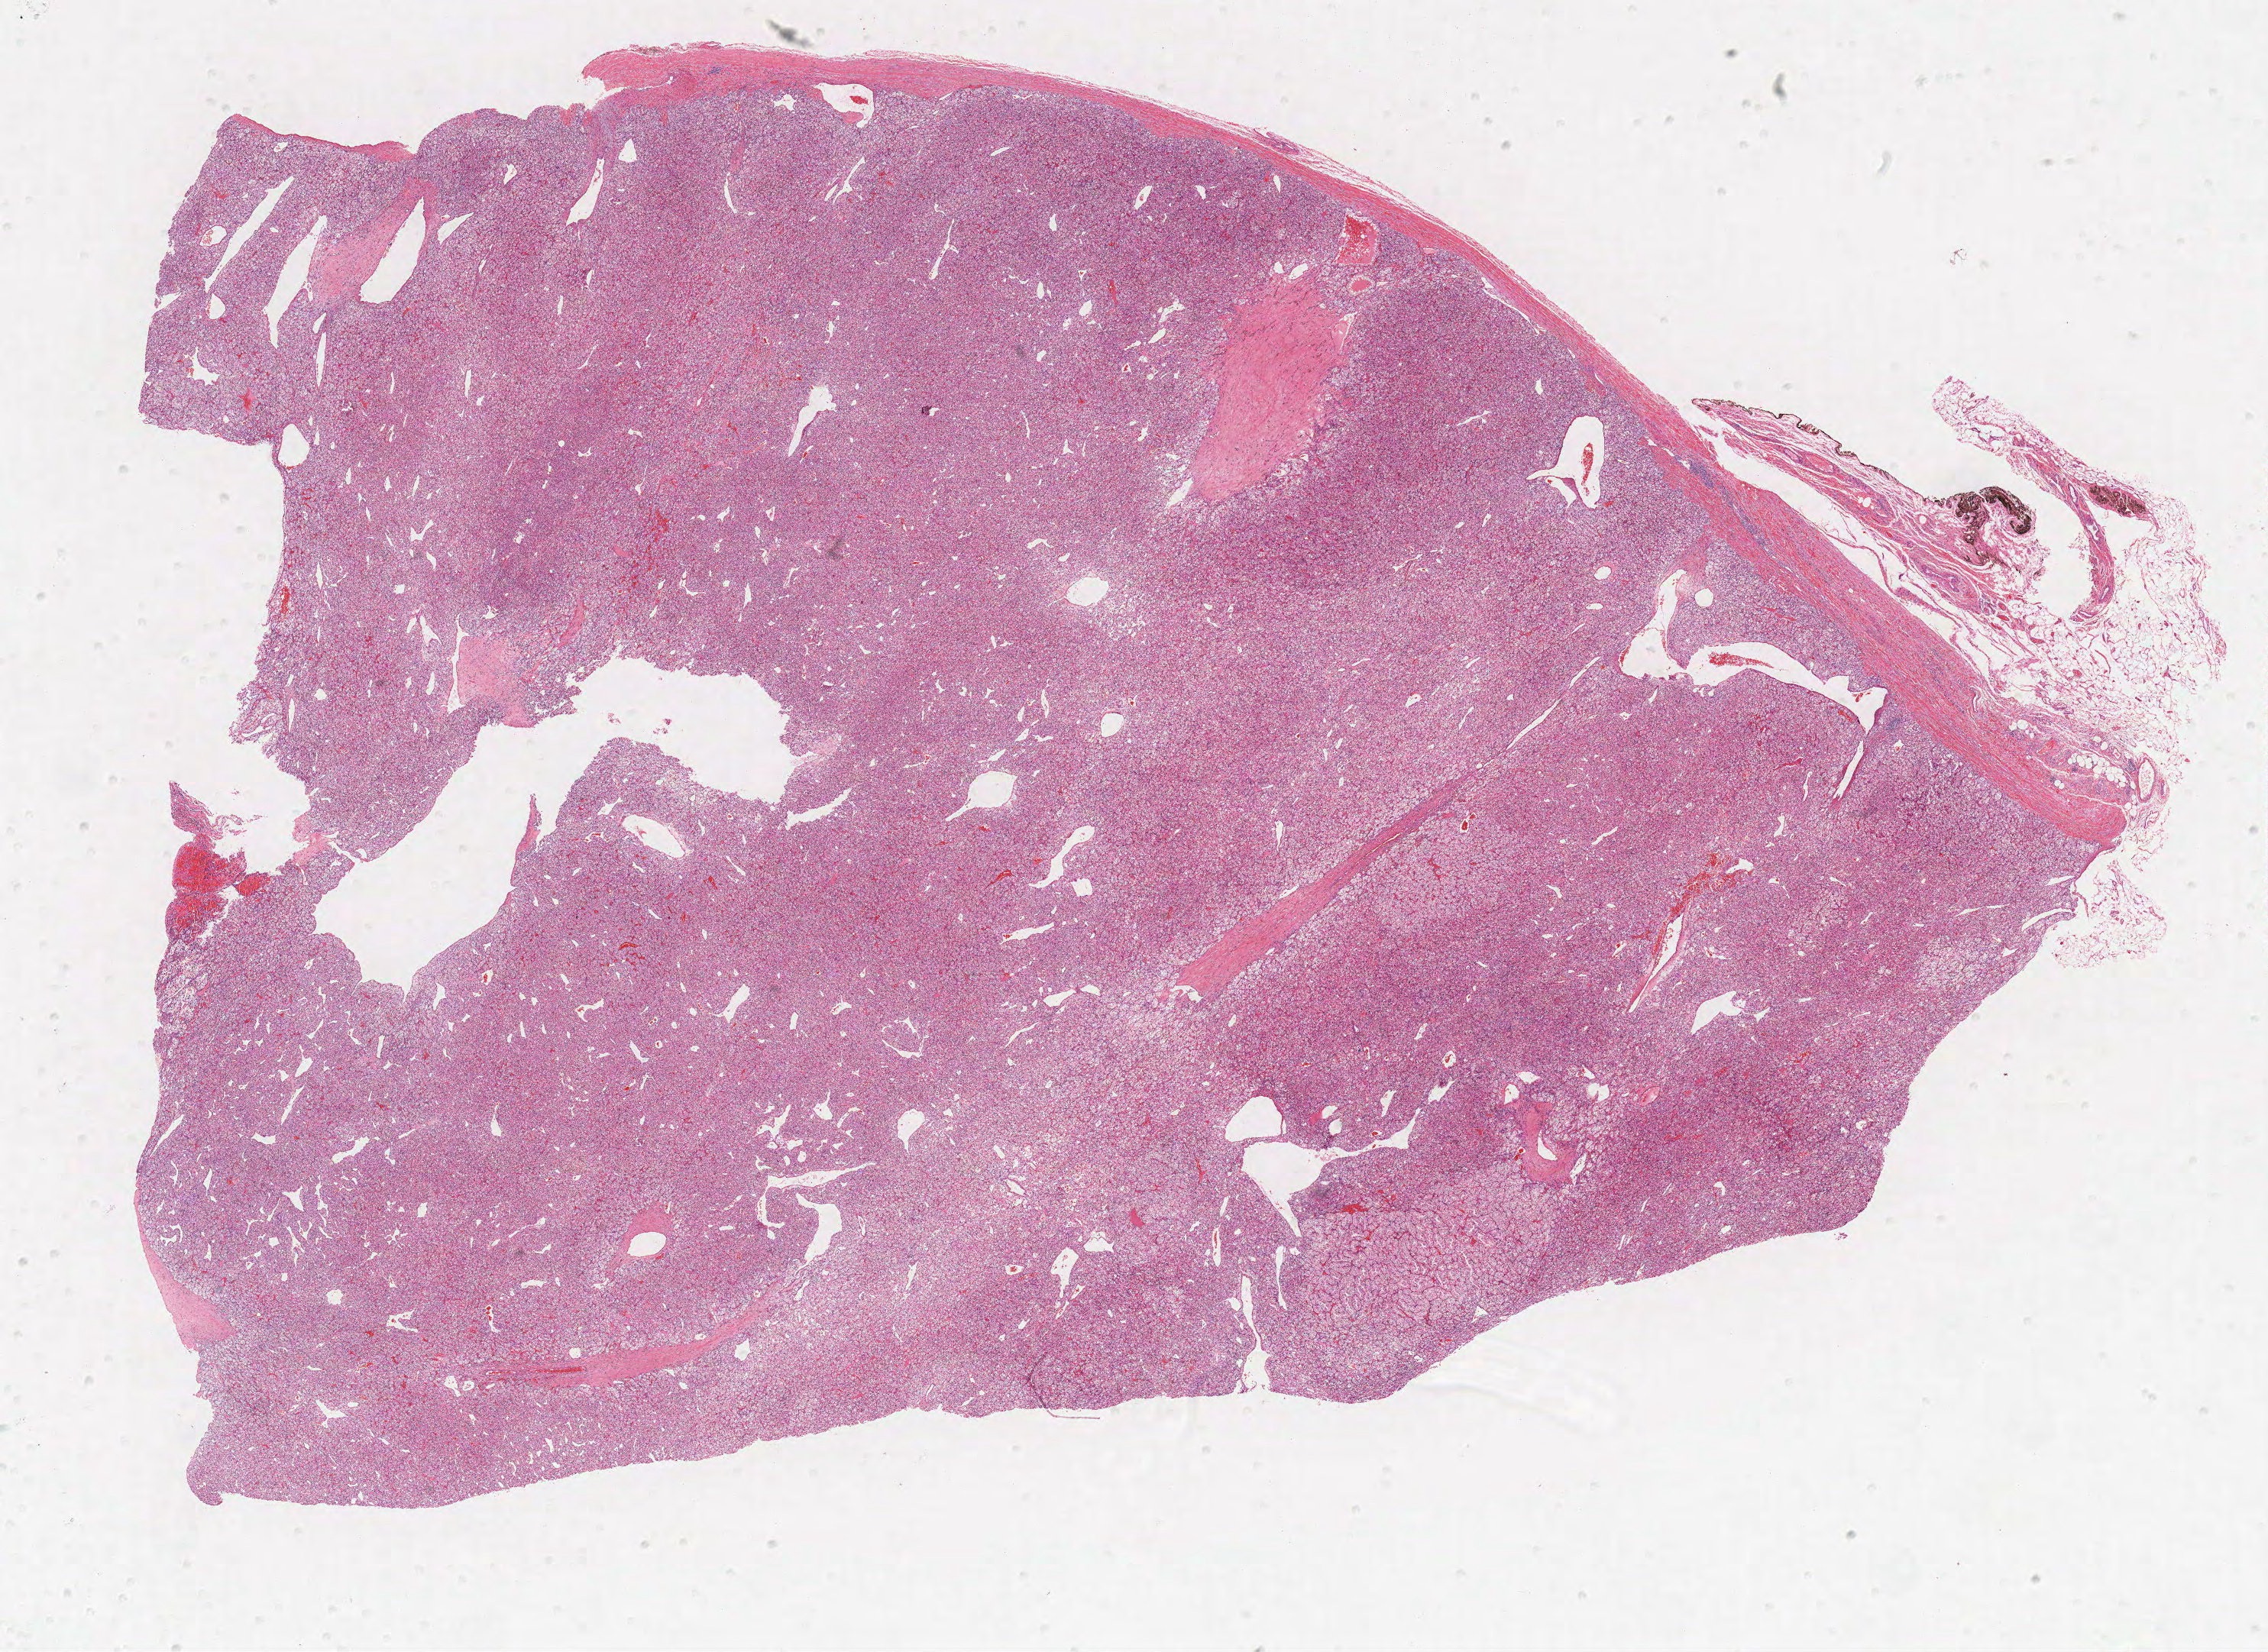
Whole-slide histology image, H&E — shown as a low-resolution overview of the whole scanned area (about 23.7 x 17.3 mm, from a 40x scan), FFPE section, kidney, primary tumour sample. Female patient; age at initial diagnosis 70 years. Histologic grade: G2 (moderately differentiated).
* AJCC pathologic stage: I
* diagnosis: Clear cell adenocarcinoma, NOS